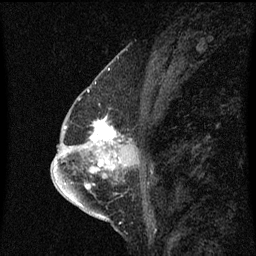
Breast MRI (dynamic contrast-enhanced), one sagittal slice. Position 34 of 60 along the scan axis. Dynamic contrast-enhanced series, image 2 of 3 at this slice position (ordered by acquisition). 1.5 T. TE 4.2 ms, TR 8.4 ms. 2 mm slice thickness. 256 × 256 image matrix, field of view 200 × 200 mm. Patient: female, 57 years. From the clinical record (not read from this slice): setting: breast cancer imaged before/during neoadjuvant chemotherapy; receptor status: HR-positive, HER2-negative.
Annotated regions visible in this slice (semi-automatically segmented with operator editing):
- analysis volume of interest (the breast-tissue region the enhancement analysis was run in; not a lesion): box from (x=88, y=118) to (x=126, y=145) px
- tumour enhancement mask (voxels above the 70 % enhancement threshold inside the analysis volume of interest): (x=92, y=118)–(x=118, y=143)